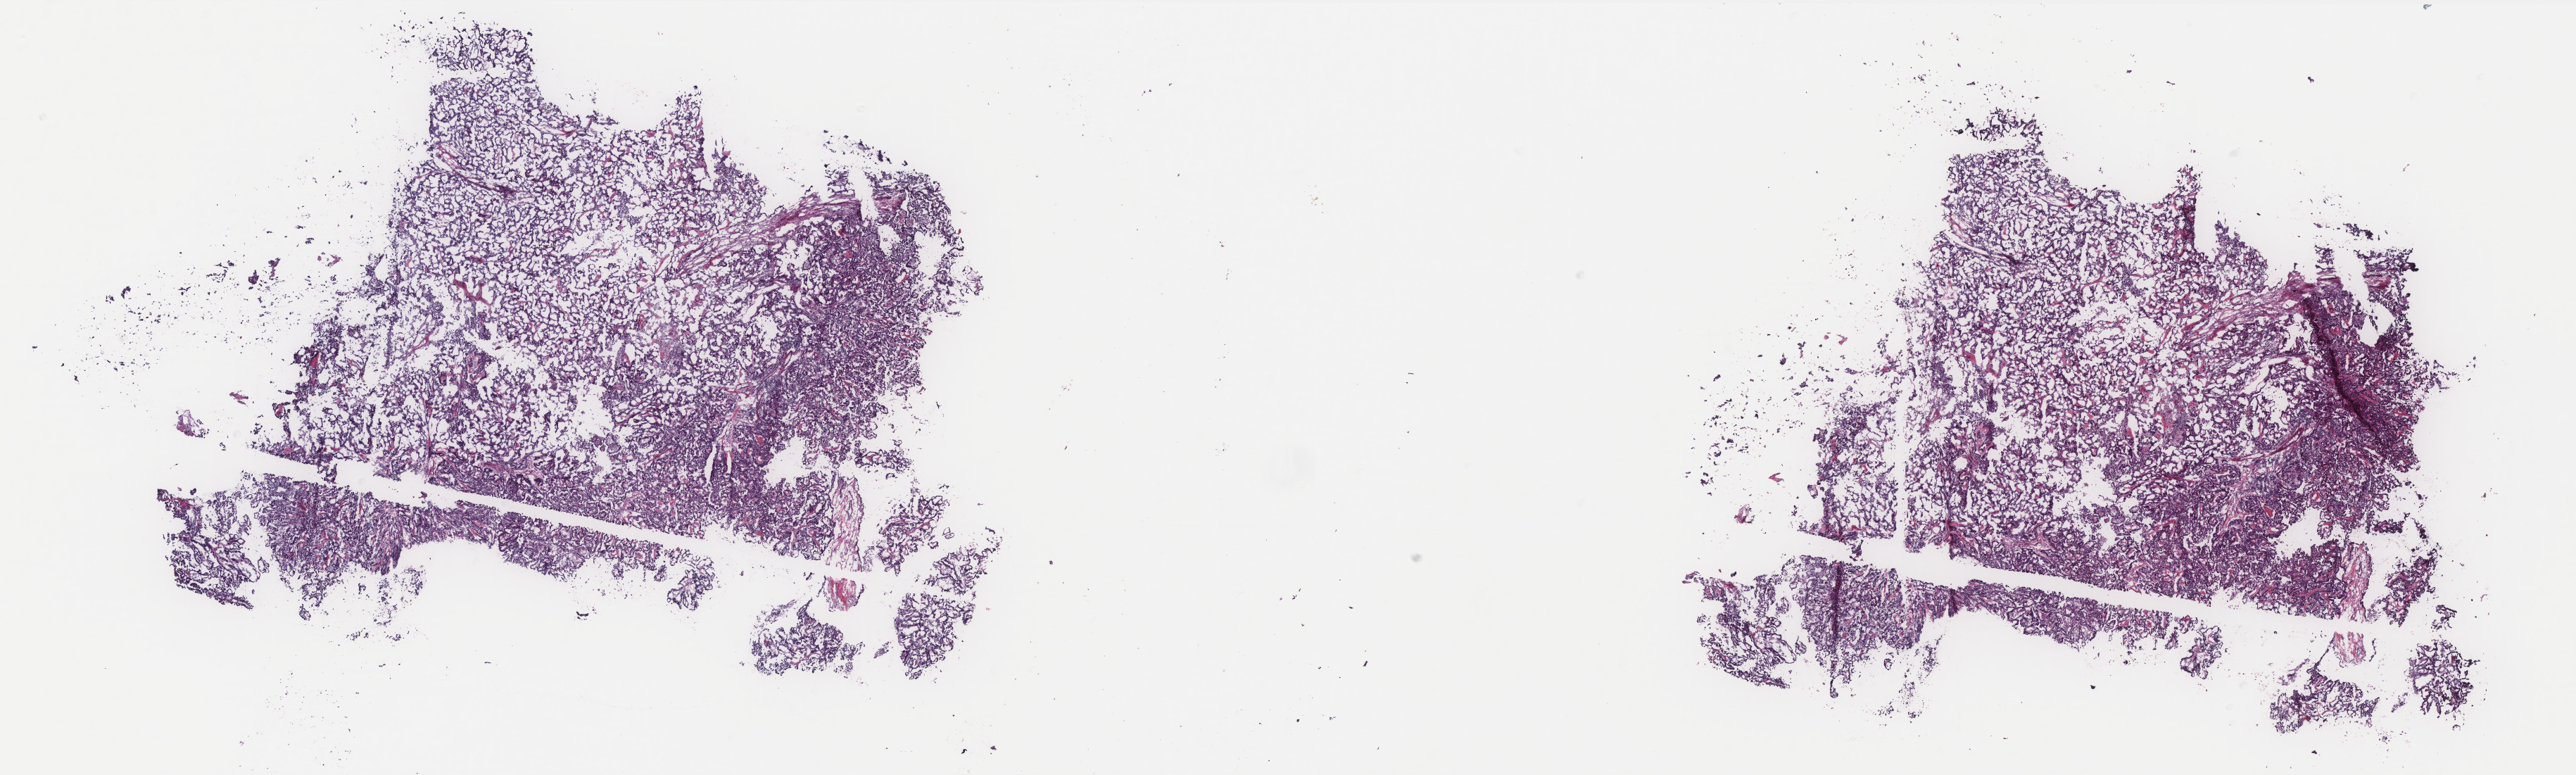
Digitized H&E-stained tissue section (whole slide) — a low-resolution overview of the entire scanned area, about 29.3 x 8.8 mm (from a 40x scan); frozen section from the bottom of the tissue portion; sample: primary tumour, thyroid. Patient: female, age at initial diagnosis 57 years. Composition of this section per pathologist review: tumour cells 80%, tumour nuclei 80%, normal cells 0%, stromal cells 20%, necrosis 0%. Inflammatory infiltration, as recorded: lymphocyte infiltration 2%, monocyte infiltration 1%, neutrophil infiltration 0%.
AJCC pathologic stage: III (7th edition). Lymph nodes positive (case pathology): 0 of 6 examined. Histologic diagnosis: Papillary carcinoma, columnar cell (thyroid gland). TNM: T3 N0 MX.